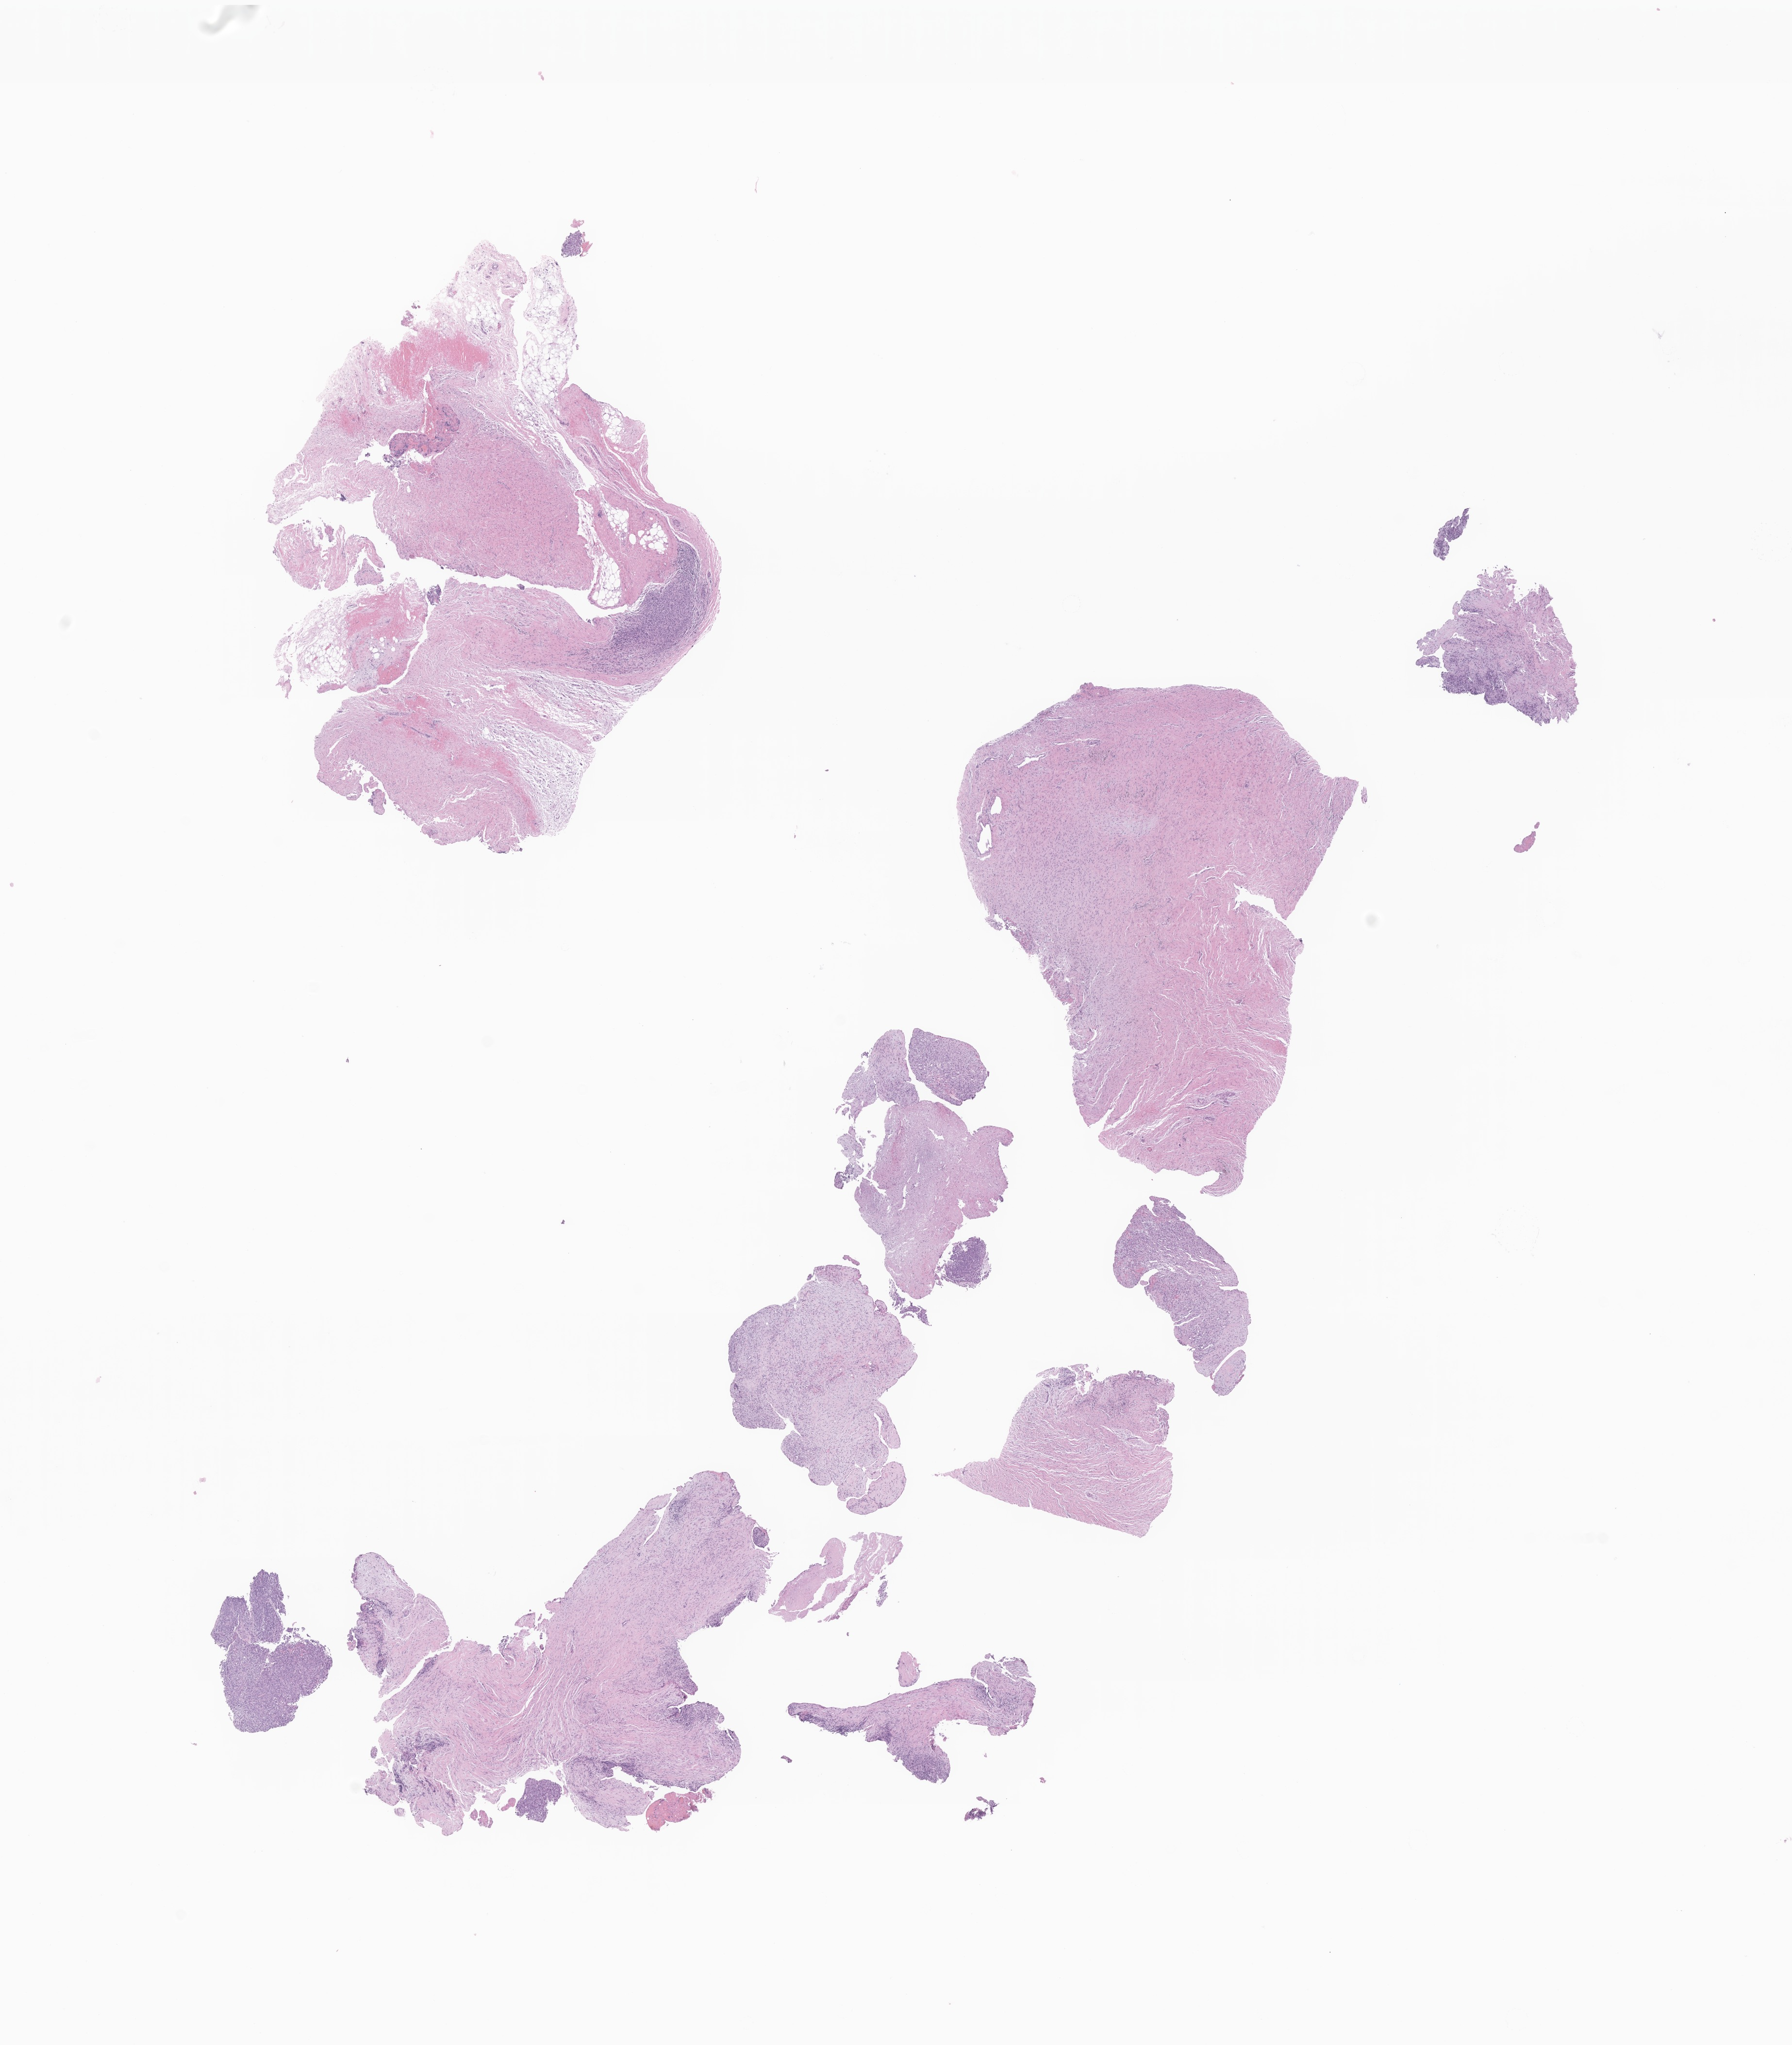
H&E whole-slide image of tumor tissue from the orbit, whole scanned area (about 15.6 x 17.8 mm) shown as a low-resolution overview. FFPE section. Patient male; age 94 months.
Diagnosis (ICD-O-3 morphology term): Sarcoma, NOS.